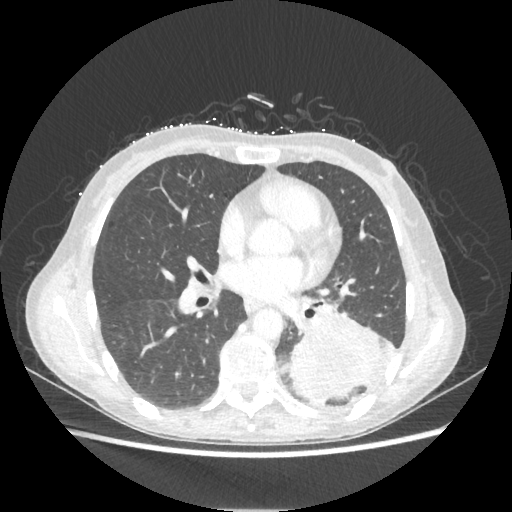
Chest CT, one axial slice. Position 109 of 221 along the scan axis. Lung window (W 1500 / L -600 HU). 512 × 512 image matrix, field of view 360 × 360 mm. Female patient, age 53 years. Case-level facts recorded for this patient, not image findings: clinical TNM (as recorded): T3 N0 M0.
Outlined on this slice (bounding box drawn by a radiologist):
- lung tumour (recorded histology: adenocarcinoma): box from (x=288, y=303) to (x=390, y=402) px